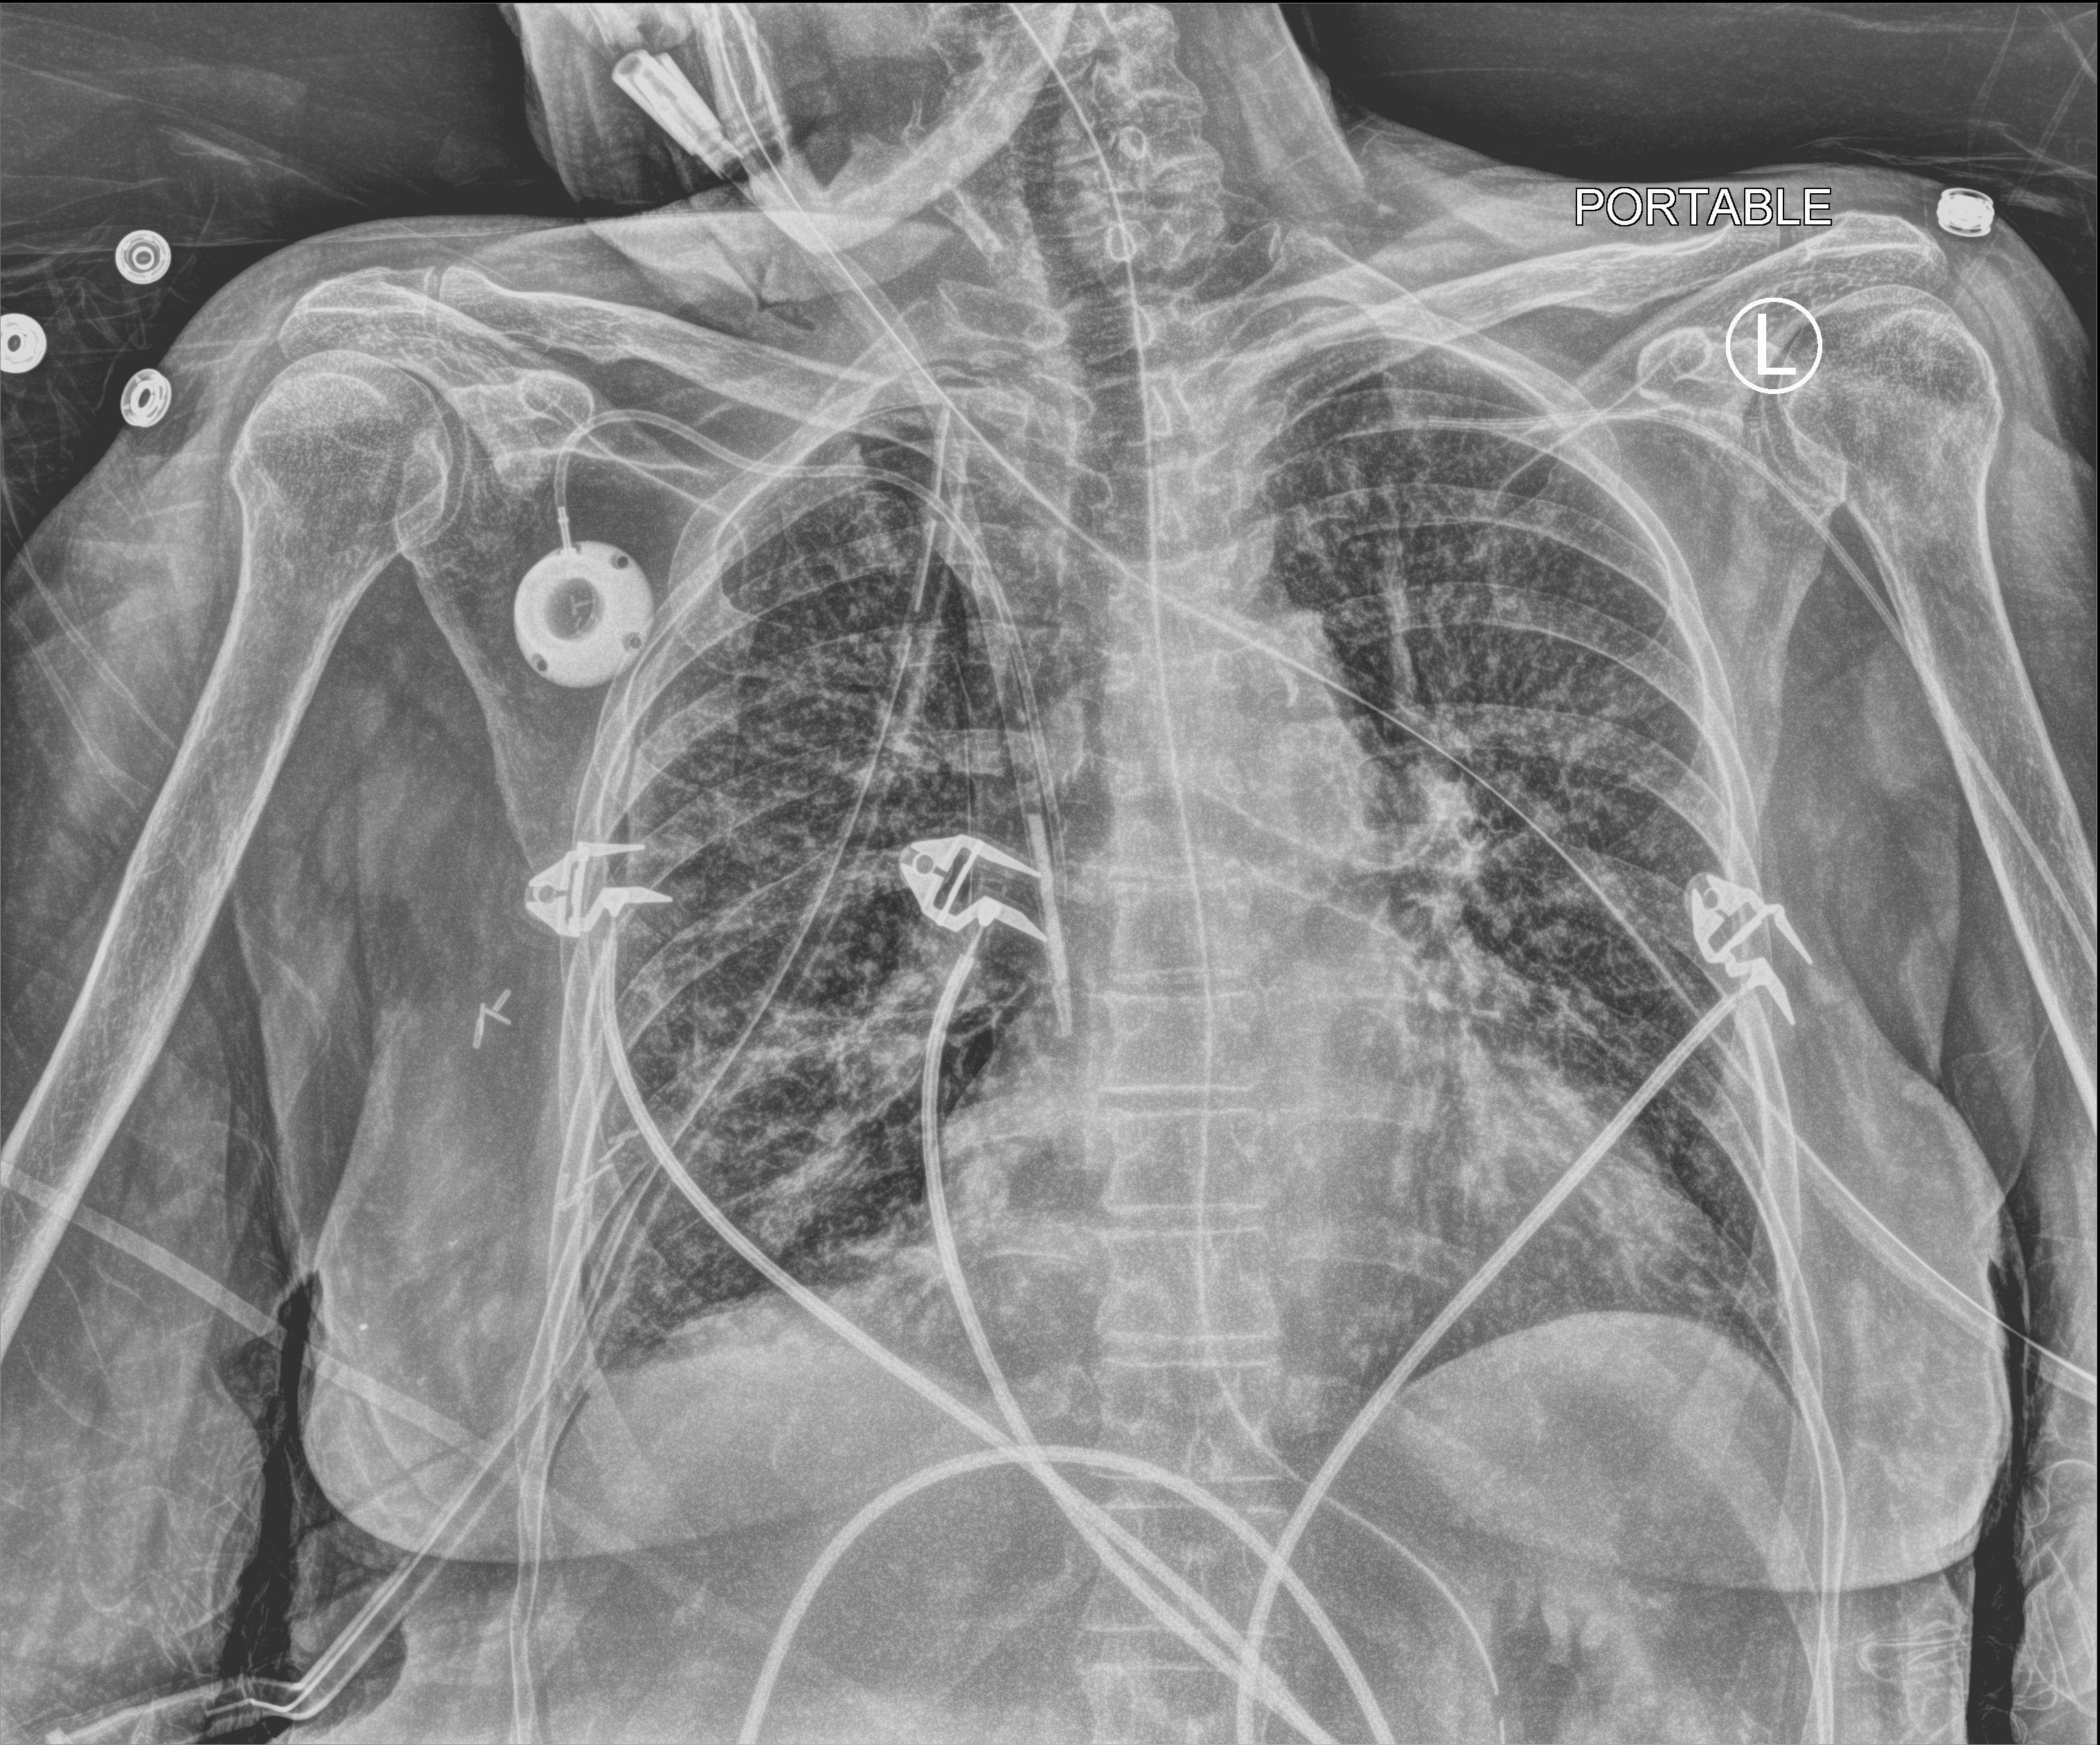
Chest X-ray (portable); anteroposterior (AP) projection. Patient hospitalised with COVID-19; female, aged 60–74 years.
Hospital-stay facts (about this admission, not read from this image; timing relative to this image not recorded): mechanically ventilated during this hospital stay: yes.